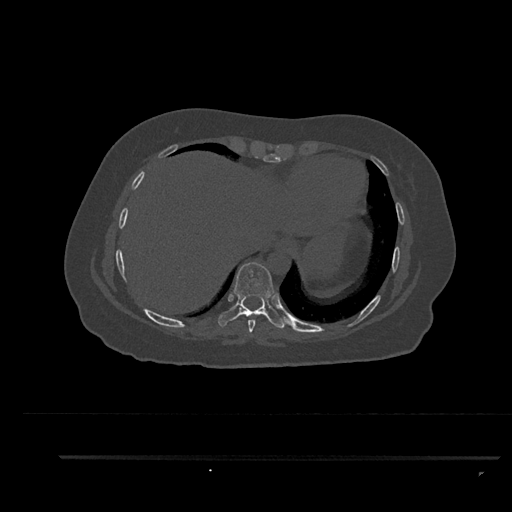
CT including the spine, one axial slice. Position 425 of 797 along the scan axis. Reconstruction kernel Br40s/3. 120 kVp. Bone window (W 1800 / L 400 HU). 0.5 mm slice thickness. 512 × 512 image matrix. Patient: female, 44 years. From the clinical record (not read from this slice): primary cancer: renal; vertebrae with lytic lesions (as recorded): L1.
Structures marked on this image (semi-automatically segmented with operator editing):
- T8 vertebra: box from (x=248, y=313) to (x=257, y=333) px
- T9 vertebra: (x=218, y=262)–(x=286, y=328)